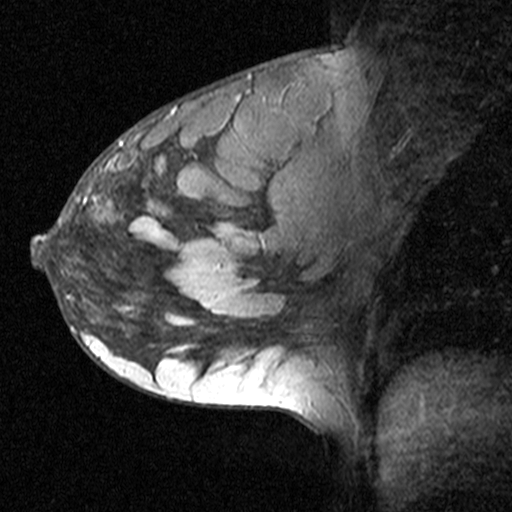
Breast MRI (dynamic contrast-enhanced), one sagittal slice. Position 25 of 44 along the scan axis. Dynamic contrast-enhanced study with each time point stored as its own series, time point 2 of 3 at this slice position (early post-contrast, ordered by acquisition time). 1.5 T. TE 4.5 ms, TR 11 ms. 3 mm slice thickness. 512 × 512 image matrix, field of view 200 × 200 mm. Female patient, age 27 years. From the clinical record (not read from this slice): setting: breast cancer imaged before/during neoadjuvant chemotherapy; receptor status: HR-positive, HER2-negative.
Annotated regions visible in this slice (semi-automatic segmentation, software-assisted and operator-edited):
- analysis volume of interest (the breast-tissue region the enhancement analysis was run in; not a lesion): bounding box [x1, y1, x2, y2] px = [36, 162, 163, 271]
- tumour enhancement mask (voxels above the 90 % enhancement threshold inside the analysis volume of interest): [40, 195, 122, 241]